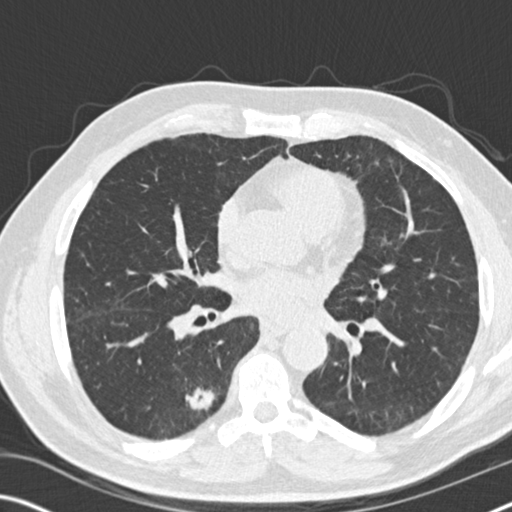
Low-dose screening chest CT, one axial slice; reconstruction kernel B30f; 120 kVp; lung window (W 1500 / L -600 HU); 2 mm slice thickness; 512 × 512 image matrix.
Outlined on this slice (manually delineated by an expert):
- lesion 1 (tumor, lower lobe of right lung): box from (x=186, y=387) to (x=215, y=411) px